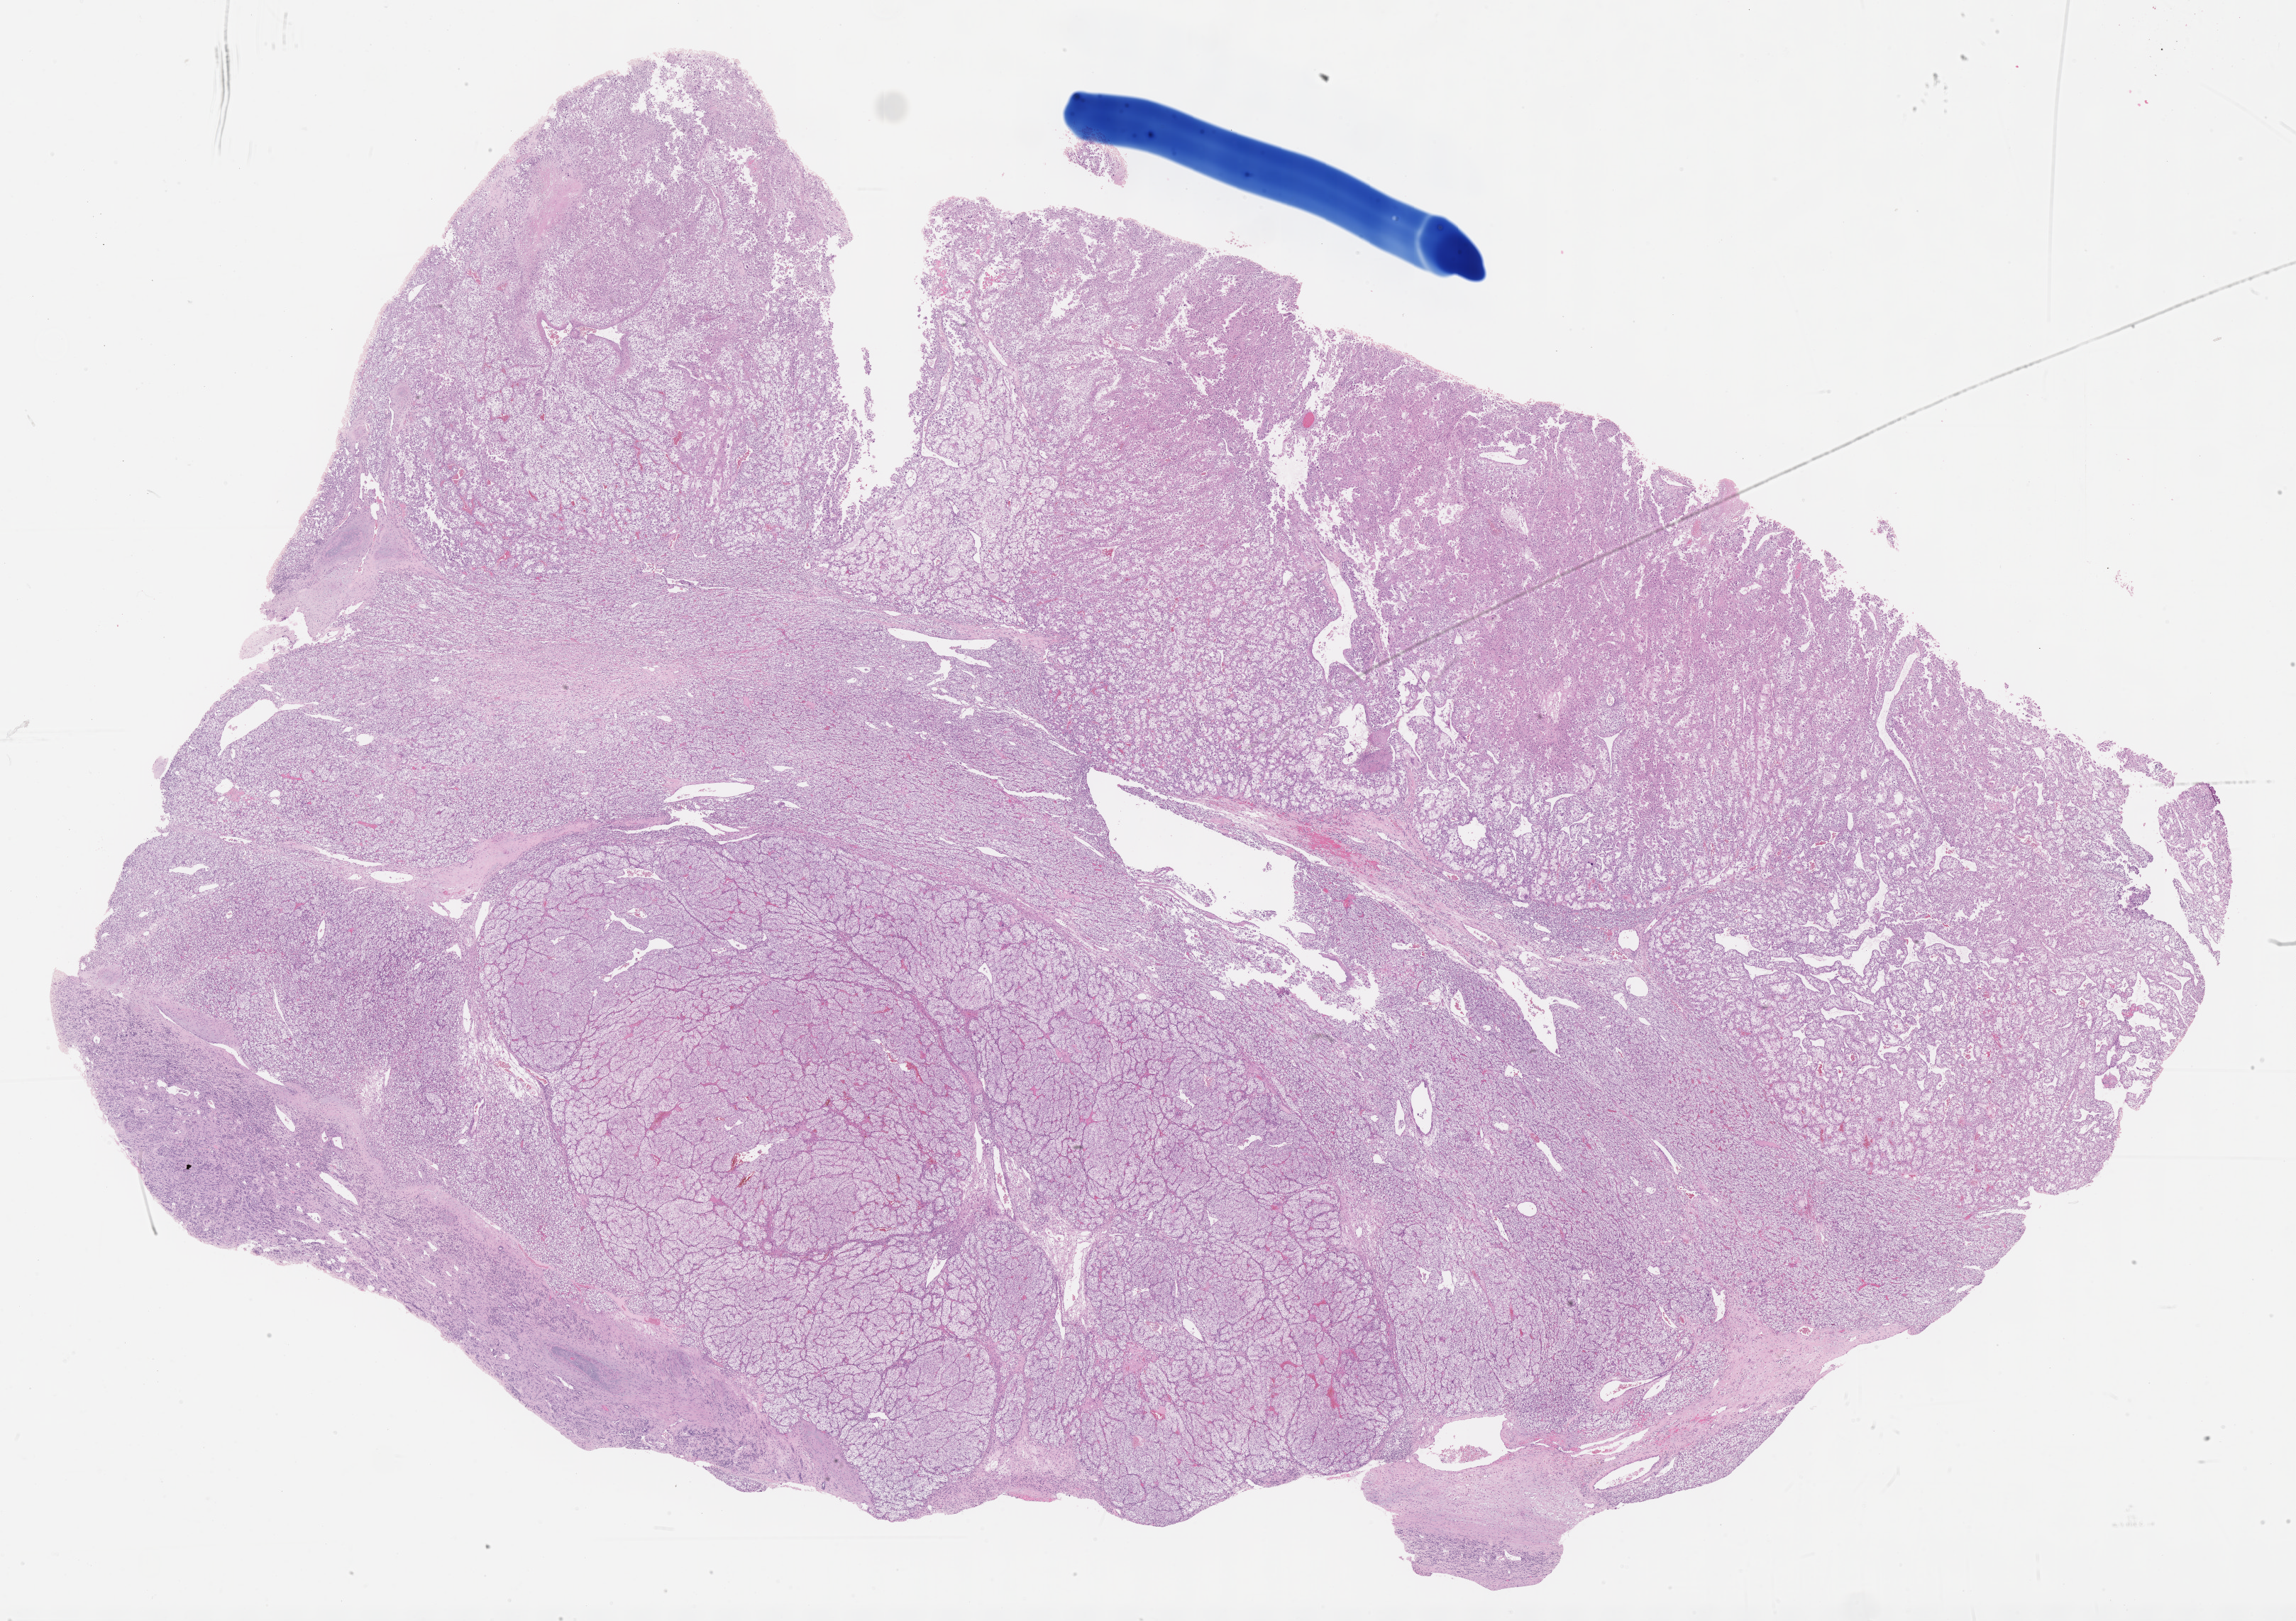
Digitized H&E-stained tissue section (whole slide) — whole scanned area (about 26.2 x 18.5 mm) shown as a low-resolution overview, FFPE section, sample: primary tumour, kidney. Patient: female, age at initial diagnosis 45 years. Histologic grade: G4 (undifferentiated).
• histologic diagnosis: Clear cell adenocarcinoma, NOS
• TNM: T3a NX M0
• AJCC pathologic stage: III